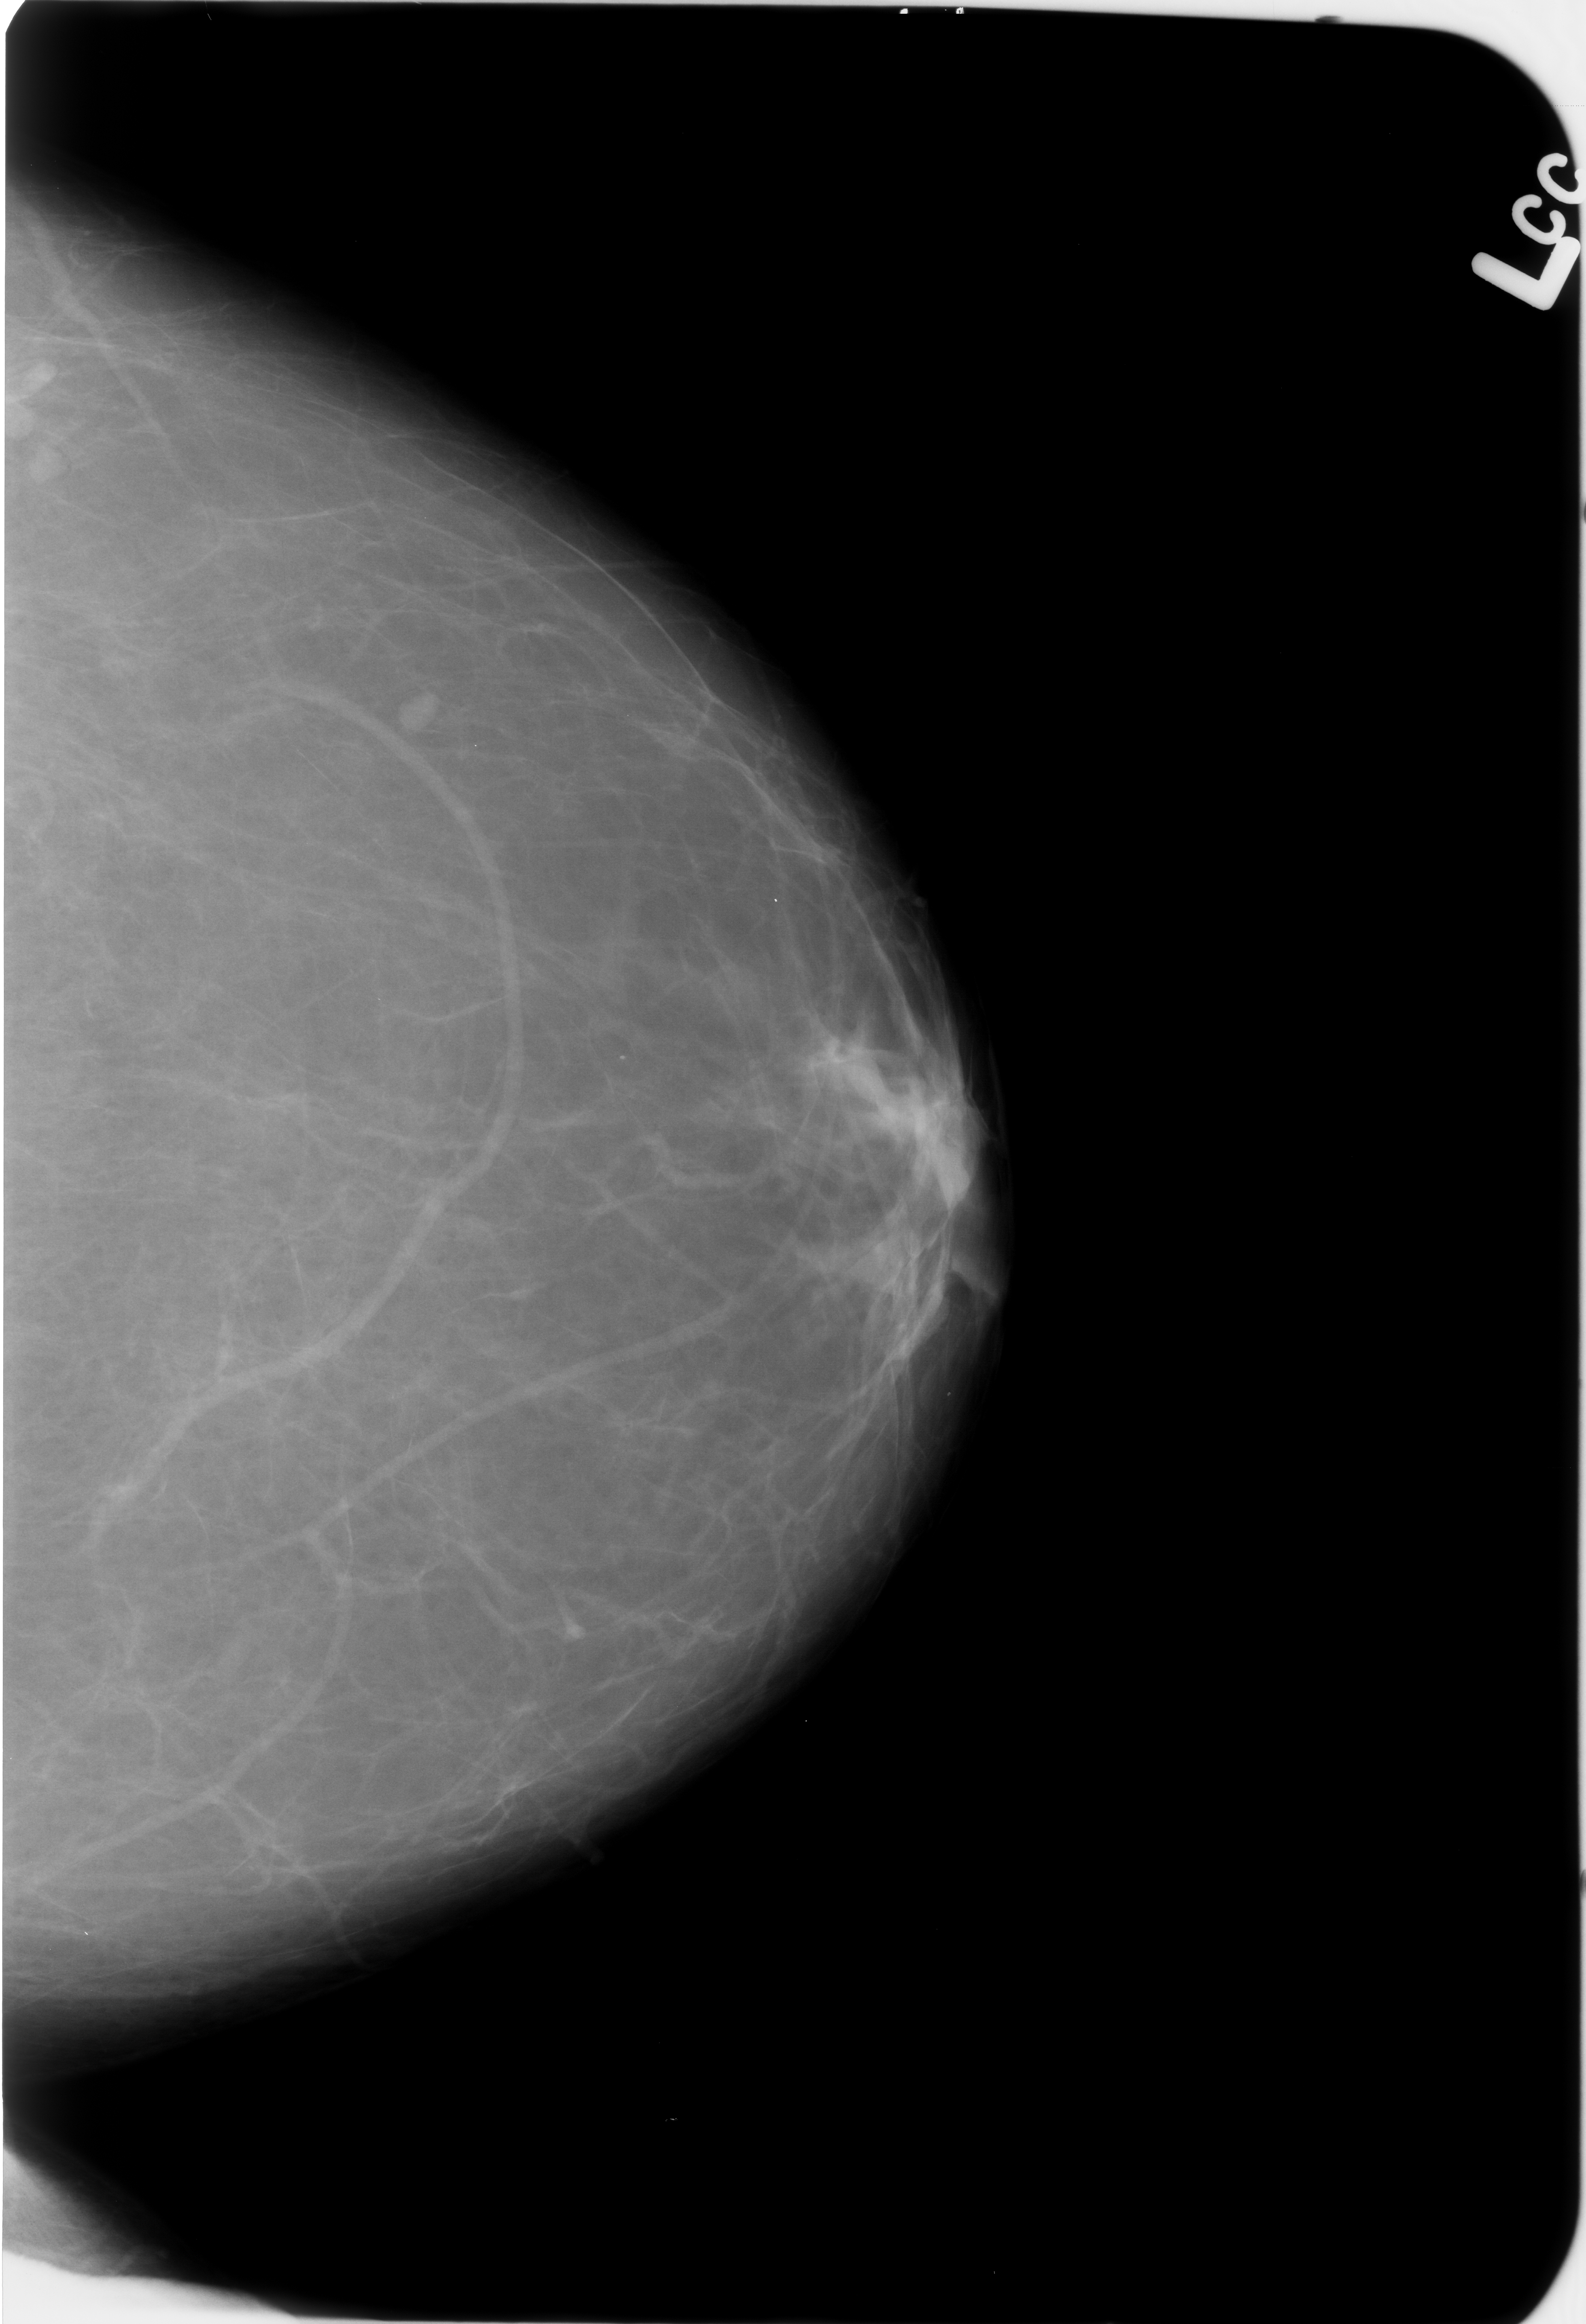
Mammogram (digitized film), left breast, craniocaudal (CC) view, BI-RADS breast density category 1 (scale 1–4).
Radiologist-marked abnormalities on this image: Finding 1 of 3: mass, shape lymph node, margins circumscribed; BI-RADS assessment category 2; subtlety rating 4 on a 1 (subtle) to 5 (obvious) scale; benign; no additional work-up was recommended (benign without callback). Finding 2 of 3: mass, shape lymph node, margins circumscribed; BI-RADS assessment category 2; benign; no additional work-up was recommended (benign without callback). Finding 3 of 3: mass, shape lymph node, margins circumscribed; BI-RADS assessment category 2; benign without callback (not worked up further).